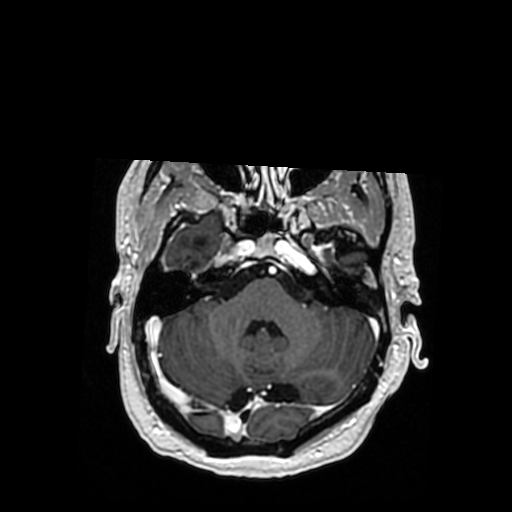
Brain MRI from a brain-tumour surgery series, one axial slice. Slice 258 of 364 in the series (ordered by position). T1-weighted post-contrast. 0.5 mm slice thickness. 512 × 512 image matrix. From the clinical record (not read from this slice): histopathology: Oligodendroglioma; WHO grade: 3; IDH mutation: yes.
Outlined on this slice (expert manual segmentation):
- previous resection cavity: bounding box (x1, y1, x2, y2) in pixels: (193, 237, 206, 266)